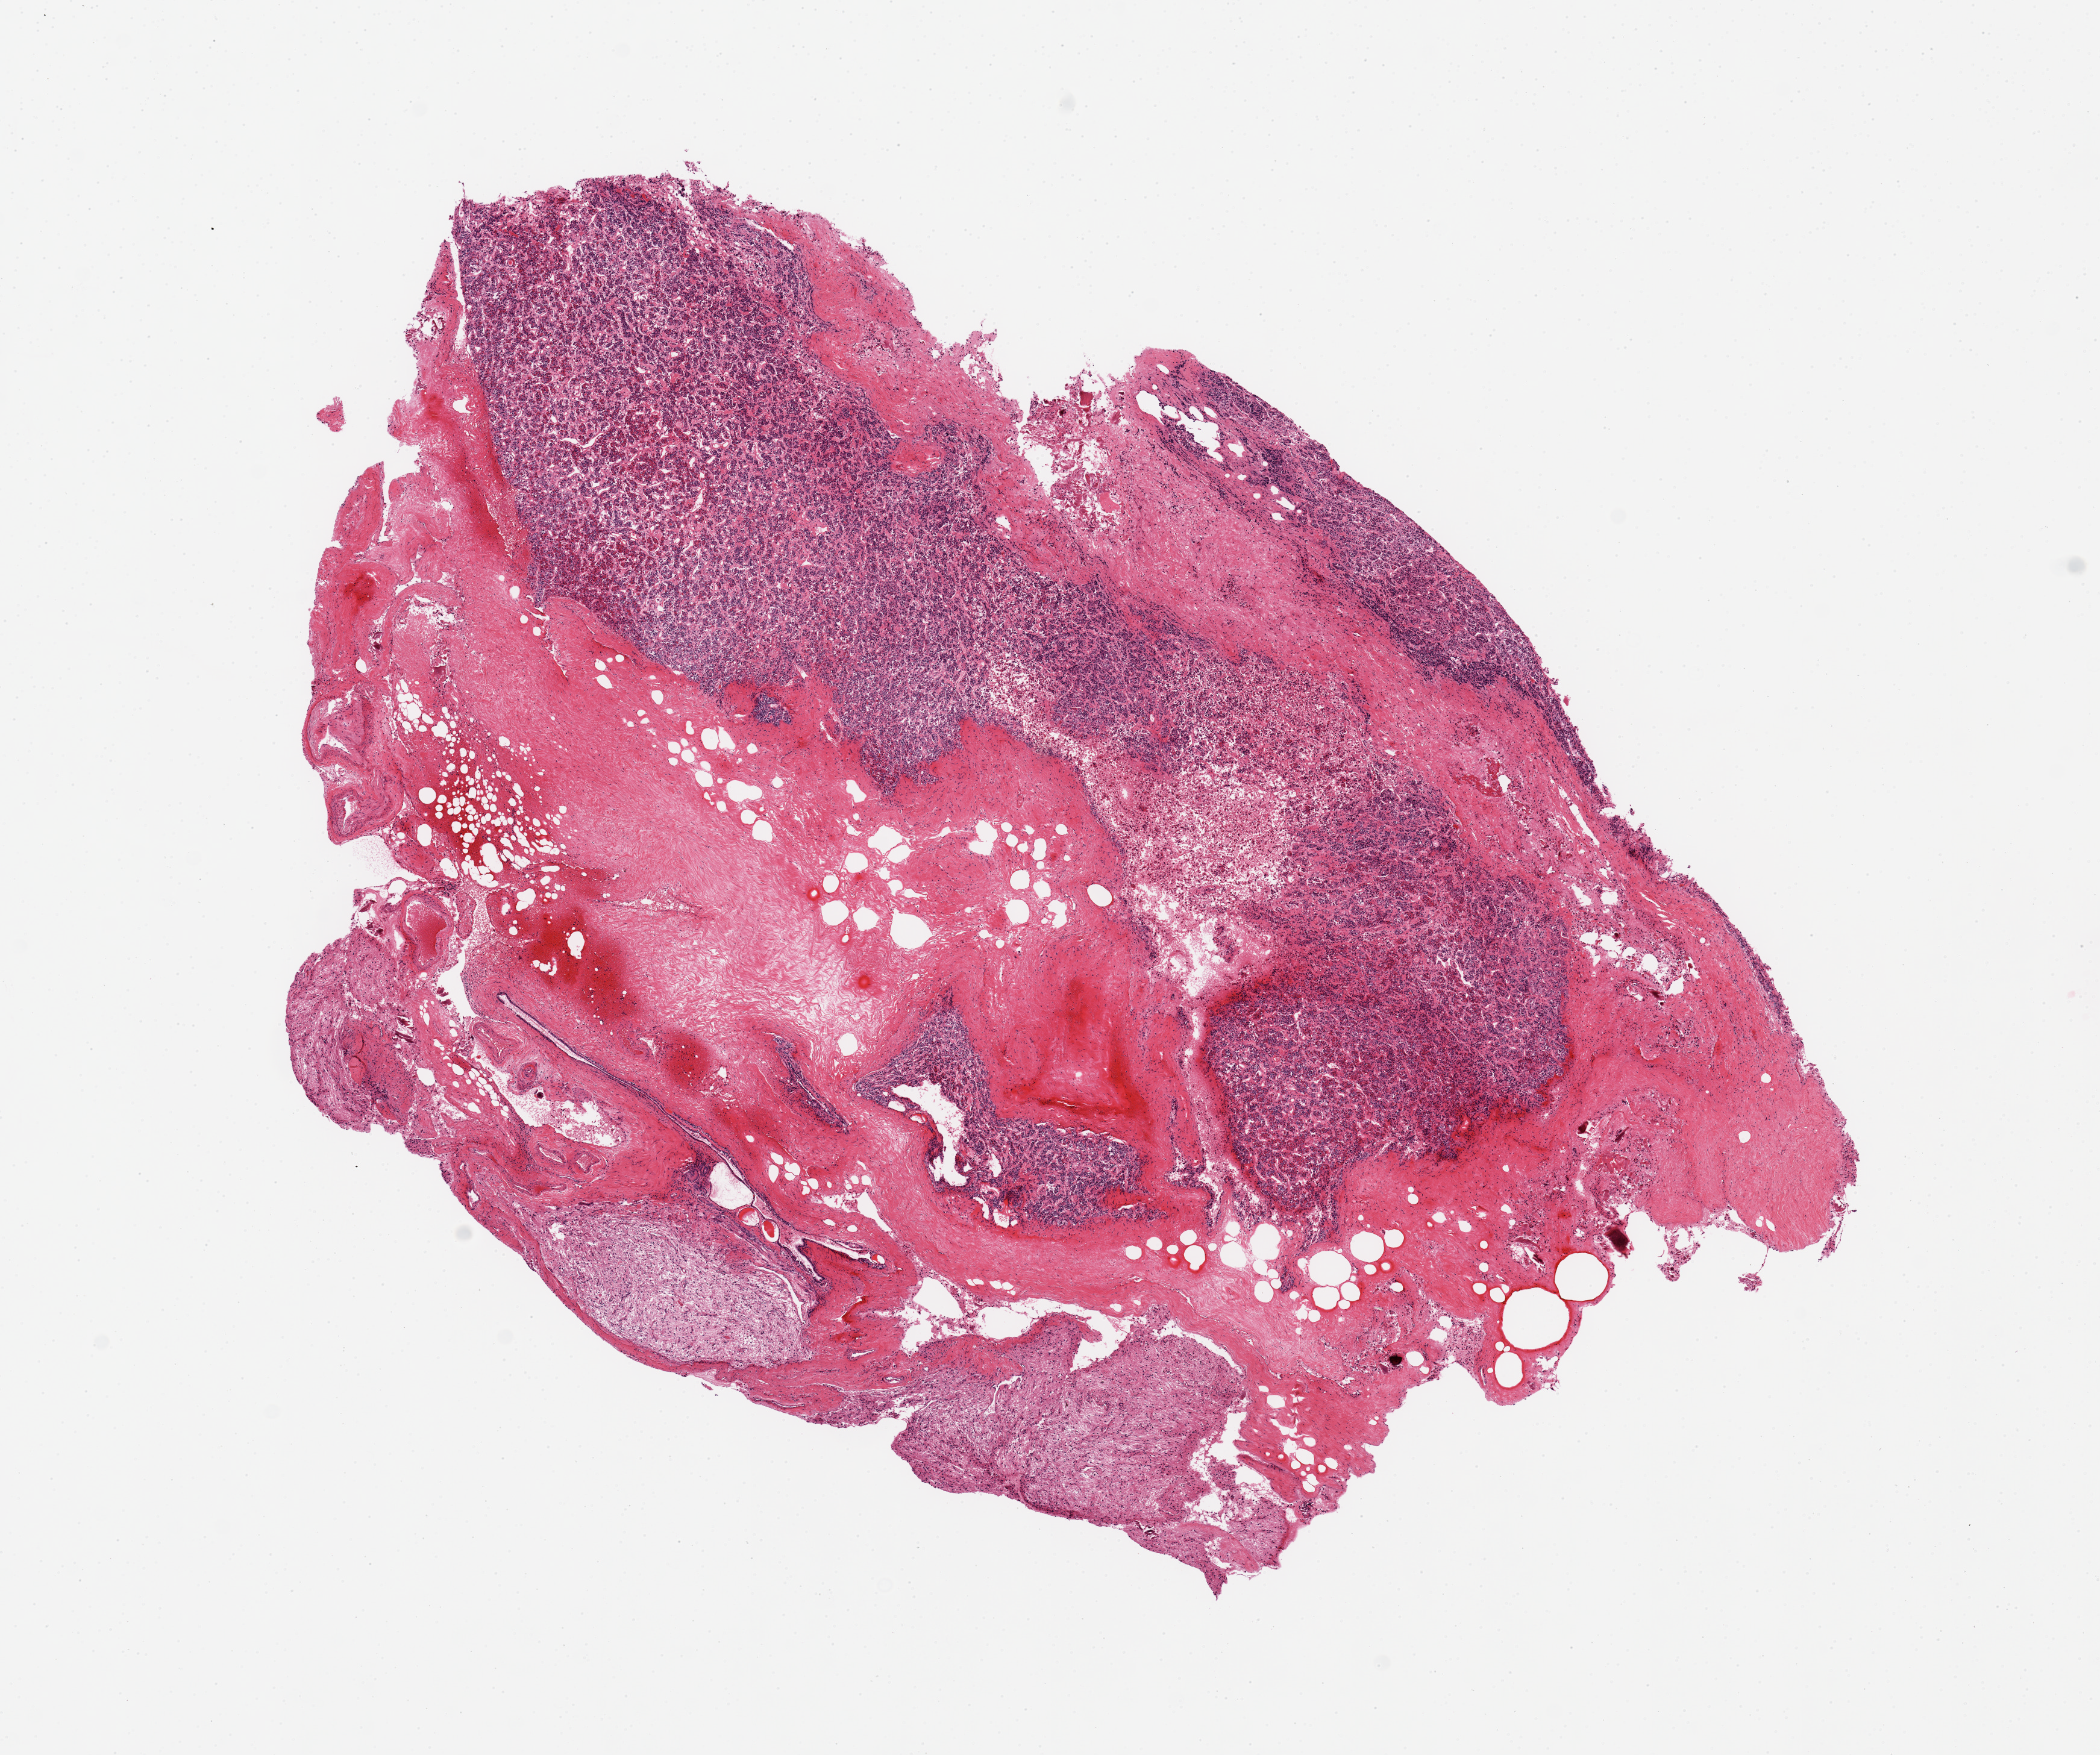
Digitized haematoxylin and eosin-stained section — shown as a low-resolution overview of the whole scanned area (about 13.8 x 11.5 mm); PAXgene-fixed paraffin-embedded (PFPE) section; sampled site (target tissue): pituitary; donor tissue sample. Donor: male.
• pathologist's review note for this sample: 1 piece, ~10% neurohypophysis; ~40% adenohypophysis; rest is dura (pink/red tissue)